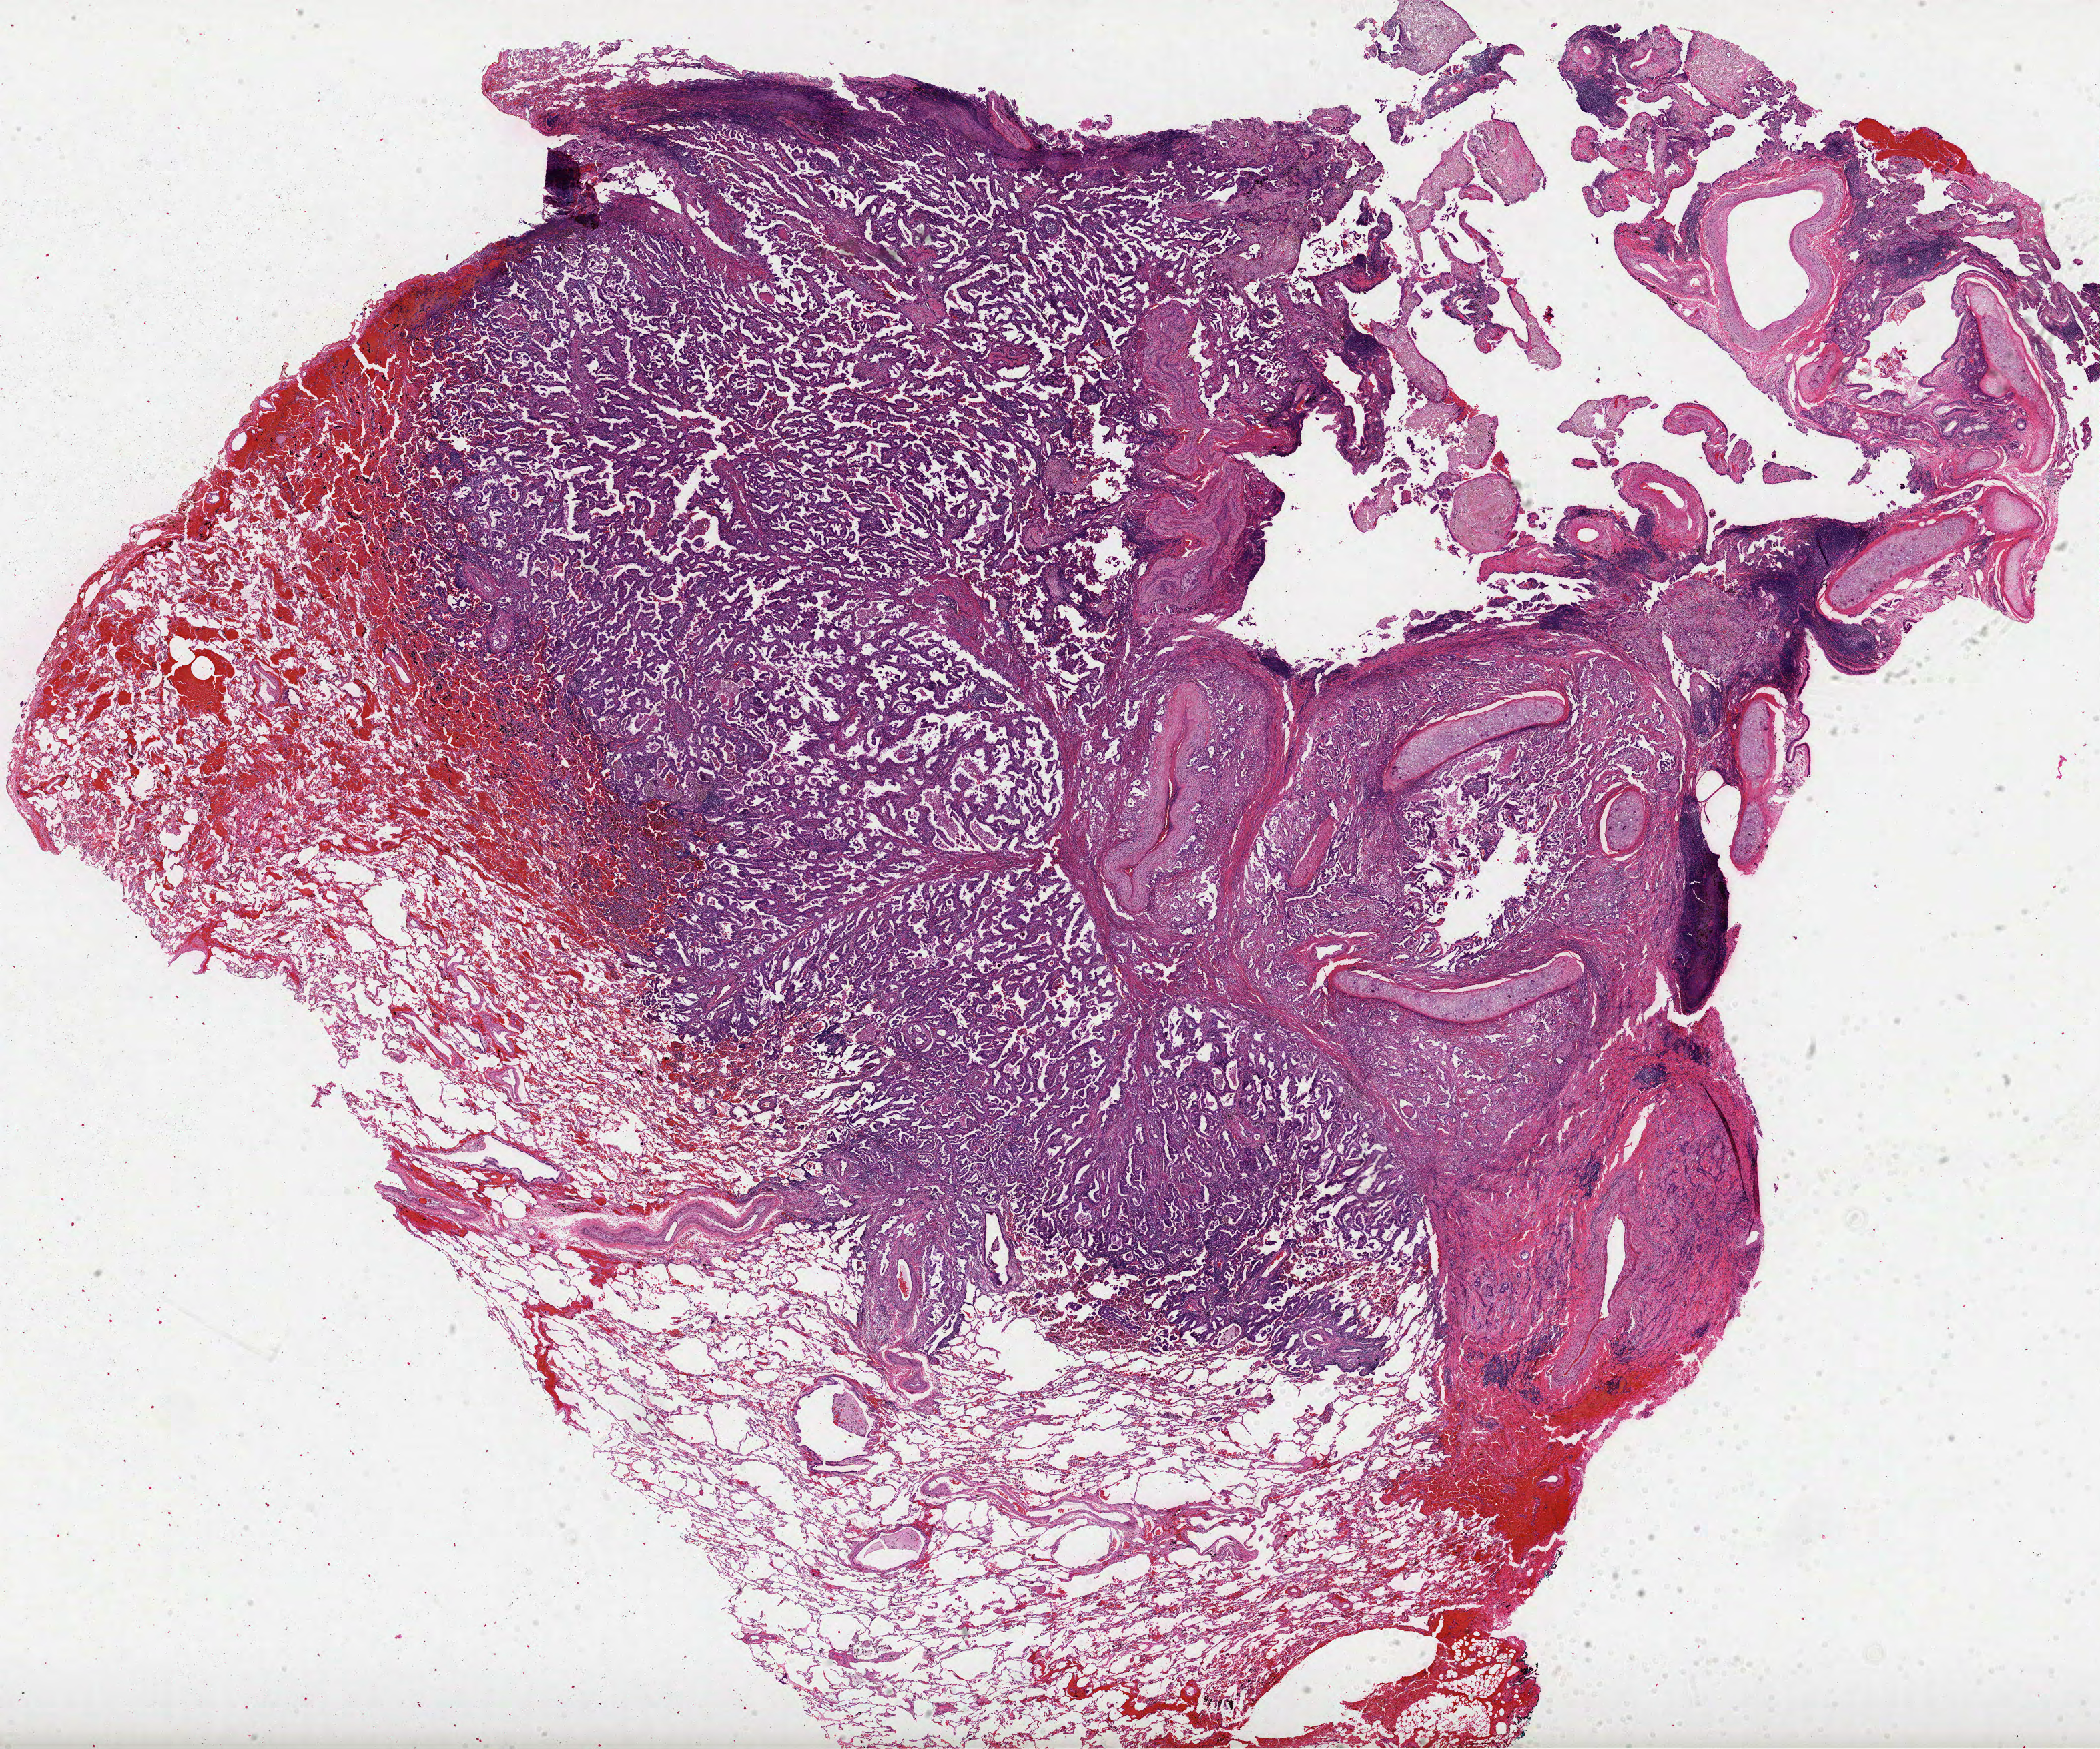
Whole-slide histology image, H&E — low-resolution overview of the scanned area, about 25.4 x 21.1 mm; FFPE section; lung, primary tumour sample. Female patient; age at initial diagnosis 64 years.
• AJCC pathologic stage: IIA (7th edition)
• histologic diagnosis: Adenocarcinoma with mixed subtypes (upper lobe, lung)